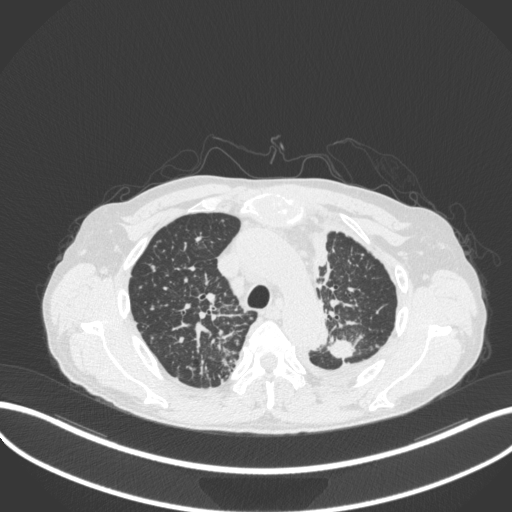
Chest CT, one axial slice; position 265 of 319 along the scan axis; 120 kVp; lung window (W 1500 / L -600 HU); 512 × 512 image matrix. Male patient, age 58 years. Case-level facts recorded for this patient, not image findings: clinical TNM (as recorded): T1c N3 M1.
Structures marked on this image (rectangle marked by the reading radiologist):
- lung tumour (recorded histology: adenocarcinoma): bounding box [x1, y1, x2, y2] px = [324, 334, 358, 359]